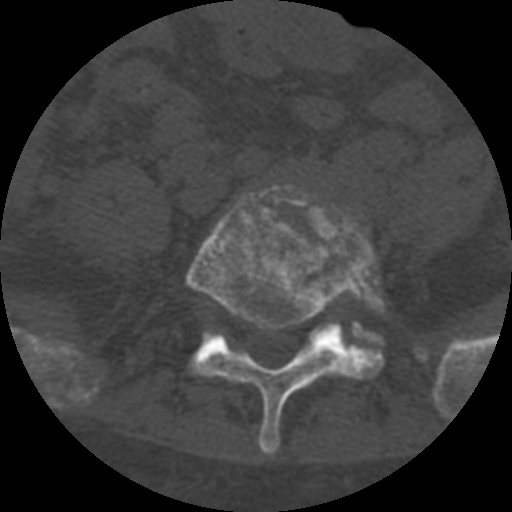
CT including the spine, one axial slice; position 183 of 708 along the scan axis; reconstruction kernel STANDARD; one of 3 acquisitions stored at this slice position; bone window (W 1800 / L 400 HU); 1.25 mm slice thickness; 512 × 512 image matrix. Patient age 55 years. From the clinical record (not read from this slice): primary cancer: colon; vertebrae with lytic lesions (as recorded): T12, L1, L5.
Structures marked on this image (semi-automatically segmented with operator editing):
- L5 vertebra: bounding box <185,185,385,455> (left, top, right, bottom; pixels)